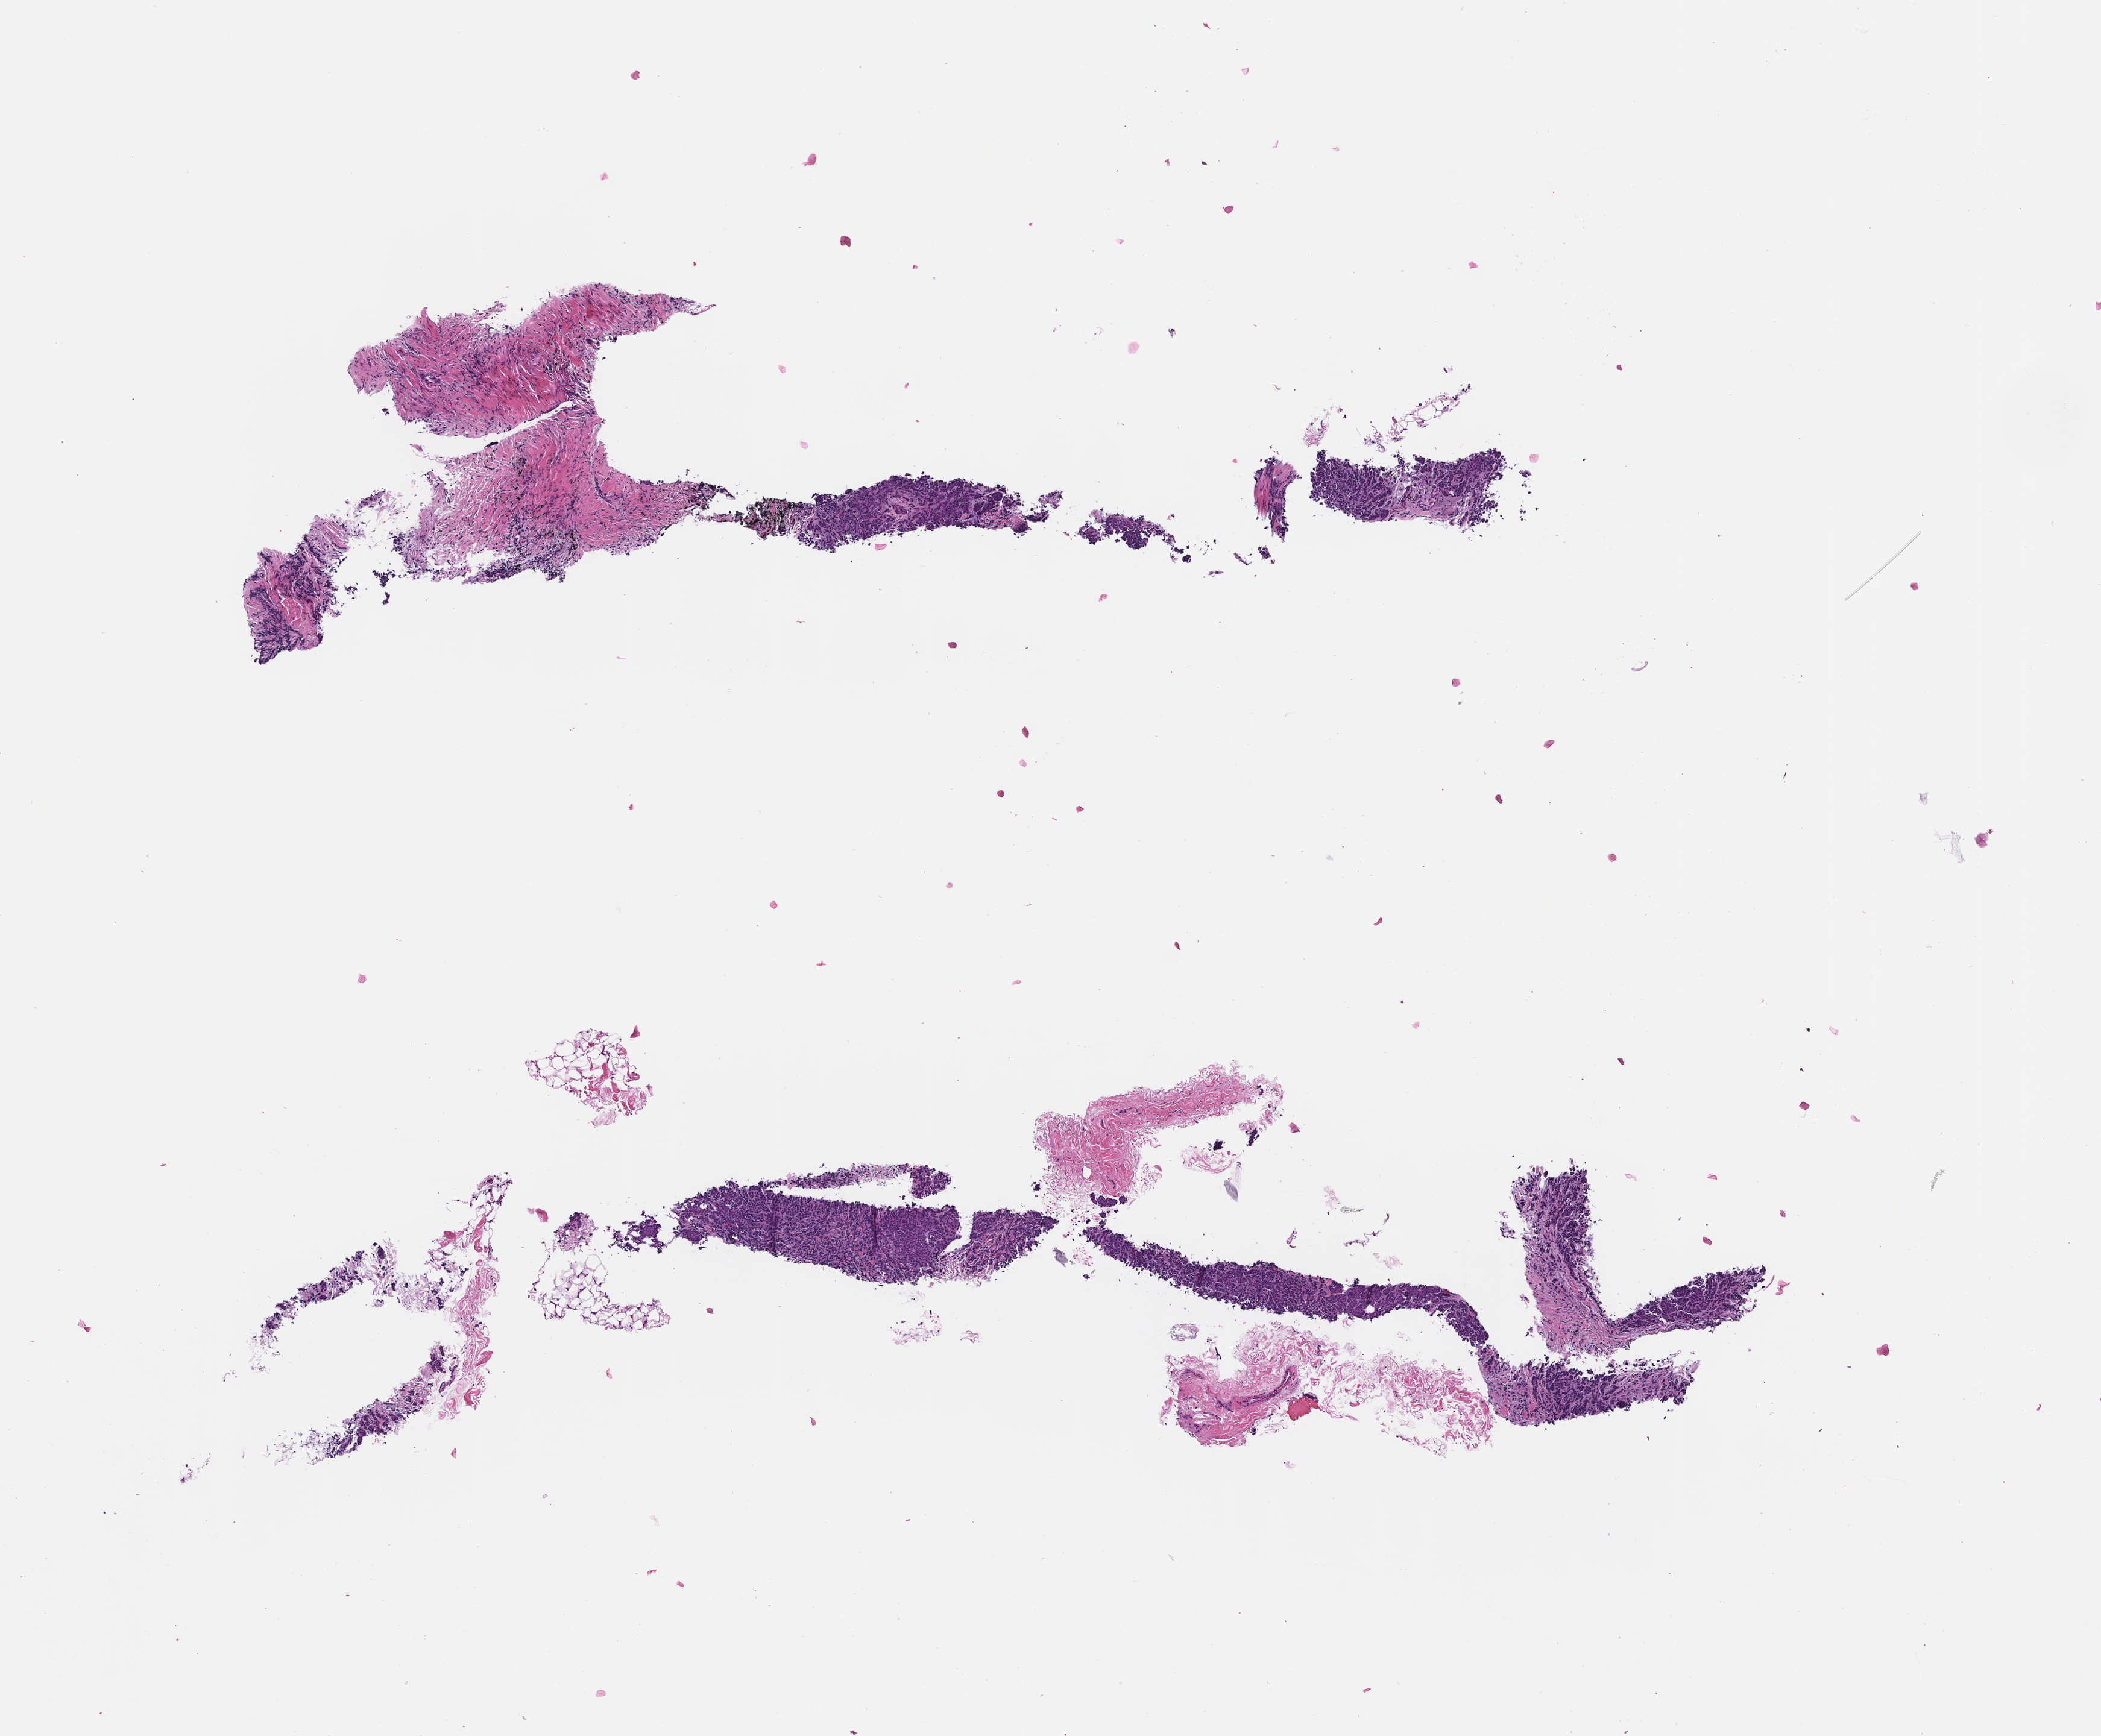
Digitized haematoxylin and eosin-stained section, a low-resolution overview of the entire scanned area, about 7.0 x 5.8 mm; formalin-fixed paraffin-embedded section; tissue site: breast; archival tissue. Female patient.
• this section: primary tumour tissue
• diagnosis: Invasive Breast Carcinoma